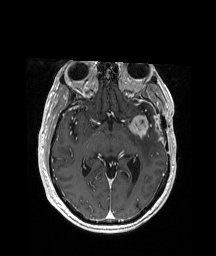
Brain MRI from a brain-tumour surgery series, one axial slice. Slice 116 of 208 in the series (ordered by position). T1-weighted post-contrast. 1 mm slice thickness. 216 × 256 image matrix, field of view 228 × 270 mm. Case-level facts recorded for this patient, not image findings: histopathology: Glioblastoma; WHO grade: 4; IDH mutation: no; tumour location: Left Anterior/Superior Temporal.
Annotated regions visible in this slice (expert manual segmentation):
- tumour: bounding box (x1, y1, x2, y2) in pixels: (123, 114, 158, 136)